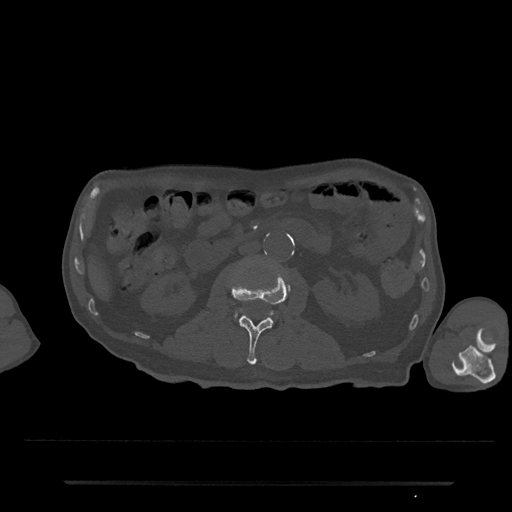
CT including the spine, one axial slice. Slice 38 of 797 in the series (ordered by position). Reconstruction kernel Br40s/3. Bone window (W 1800 / L 400 HU). 512 × 512 image matrix, field of view 427 × 427 mm. Patient: male, 74 years. From the clinical record (not read from this slice): primary cancer: prostate.
Outlined on this slice (semi-automatically segmented with operator editing):
- L2 vertebra: bounding box (x1, y1, x2, y2) in pixels: (230, 269, 291, 365)
- L3 vertebra: (234, 308, 278, 319)